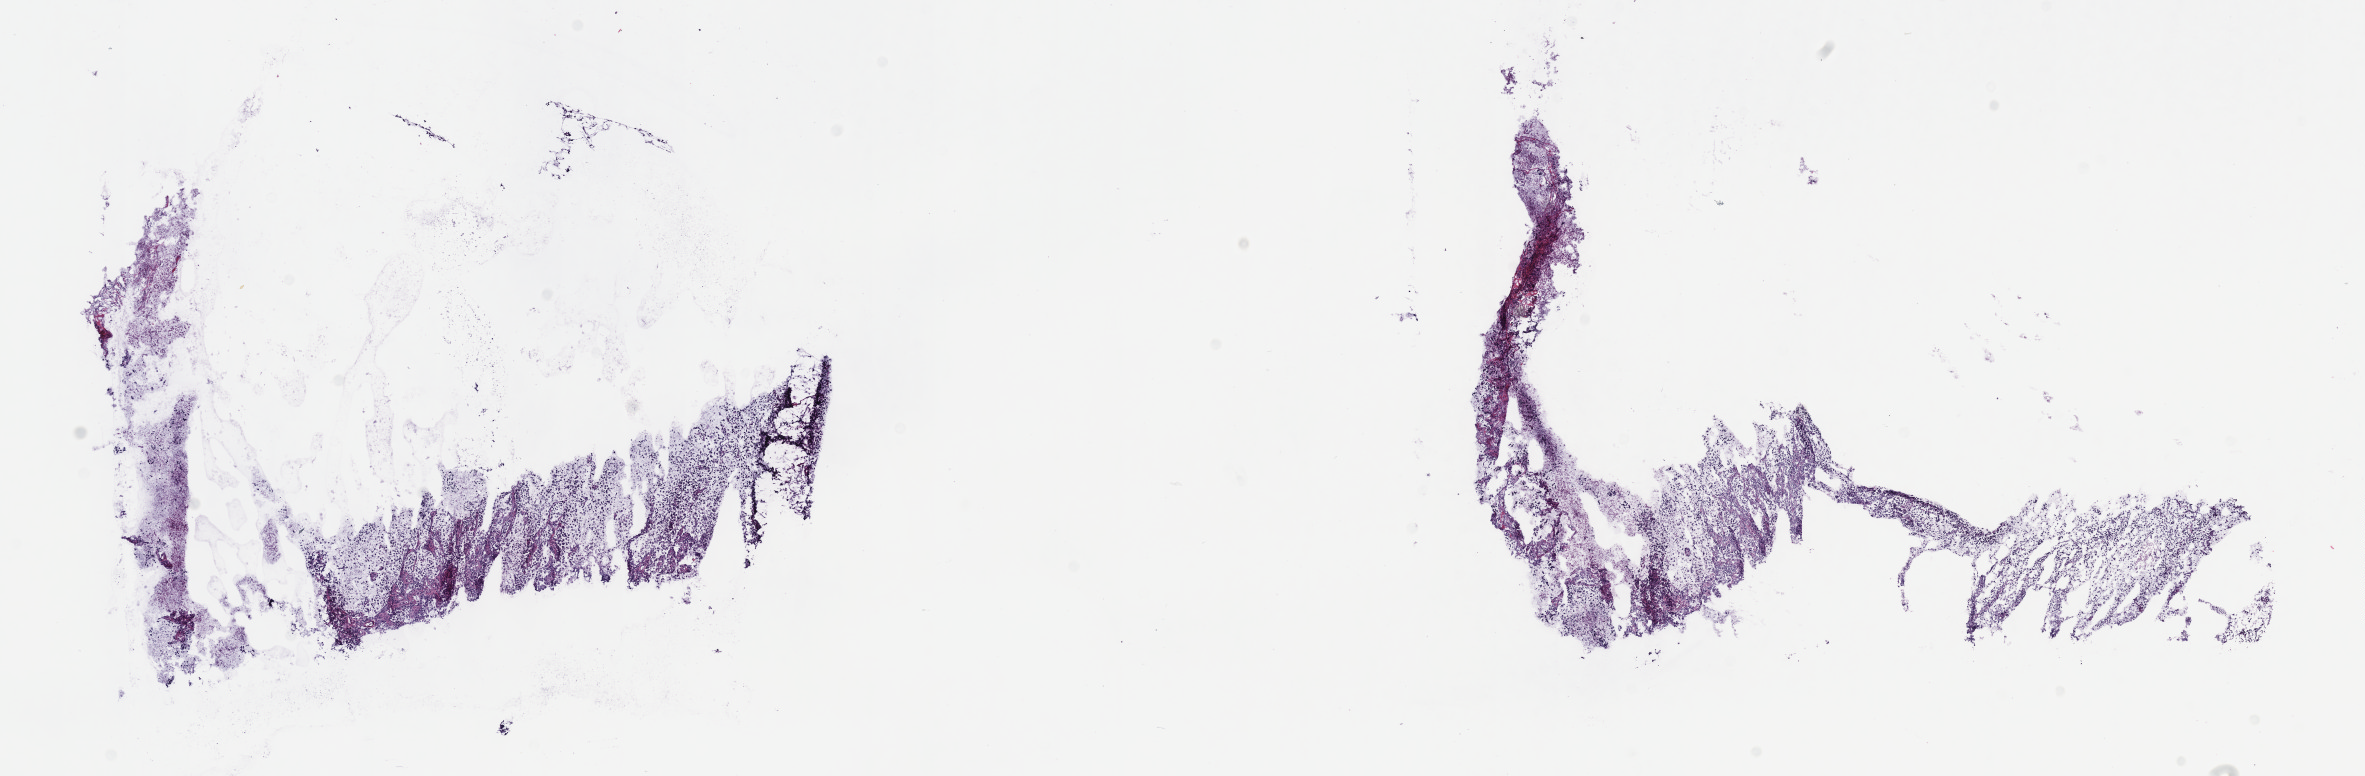
Digitized H&E-stained tissue section (whole slide), shown as a low-resolution overview of the whole scanned area (about 19.1 x 6.3 mm); frozen section from the top of the tissue portion; stomach, primary tumour sample. Male, age 67 years at initial diagnosis. Histologic grade: G1 (well differentiated). Slide review estimates, as recorded: tumour cells 80%, tumour nuclei 80%, normal cells 0%, stromal cells 20%, necrosis 0%. Infiltration values recorded for this section: lymphocyte infiltration 0%, monocyte infiltration 0%, neutrophil infiltration 0%.
- AJCC pathologic stage: IIIB (7th edition)
- diagnosis: Mucinous adenocarcinoma
- lymph nodes positive (case pathology): 11 of 29 examined